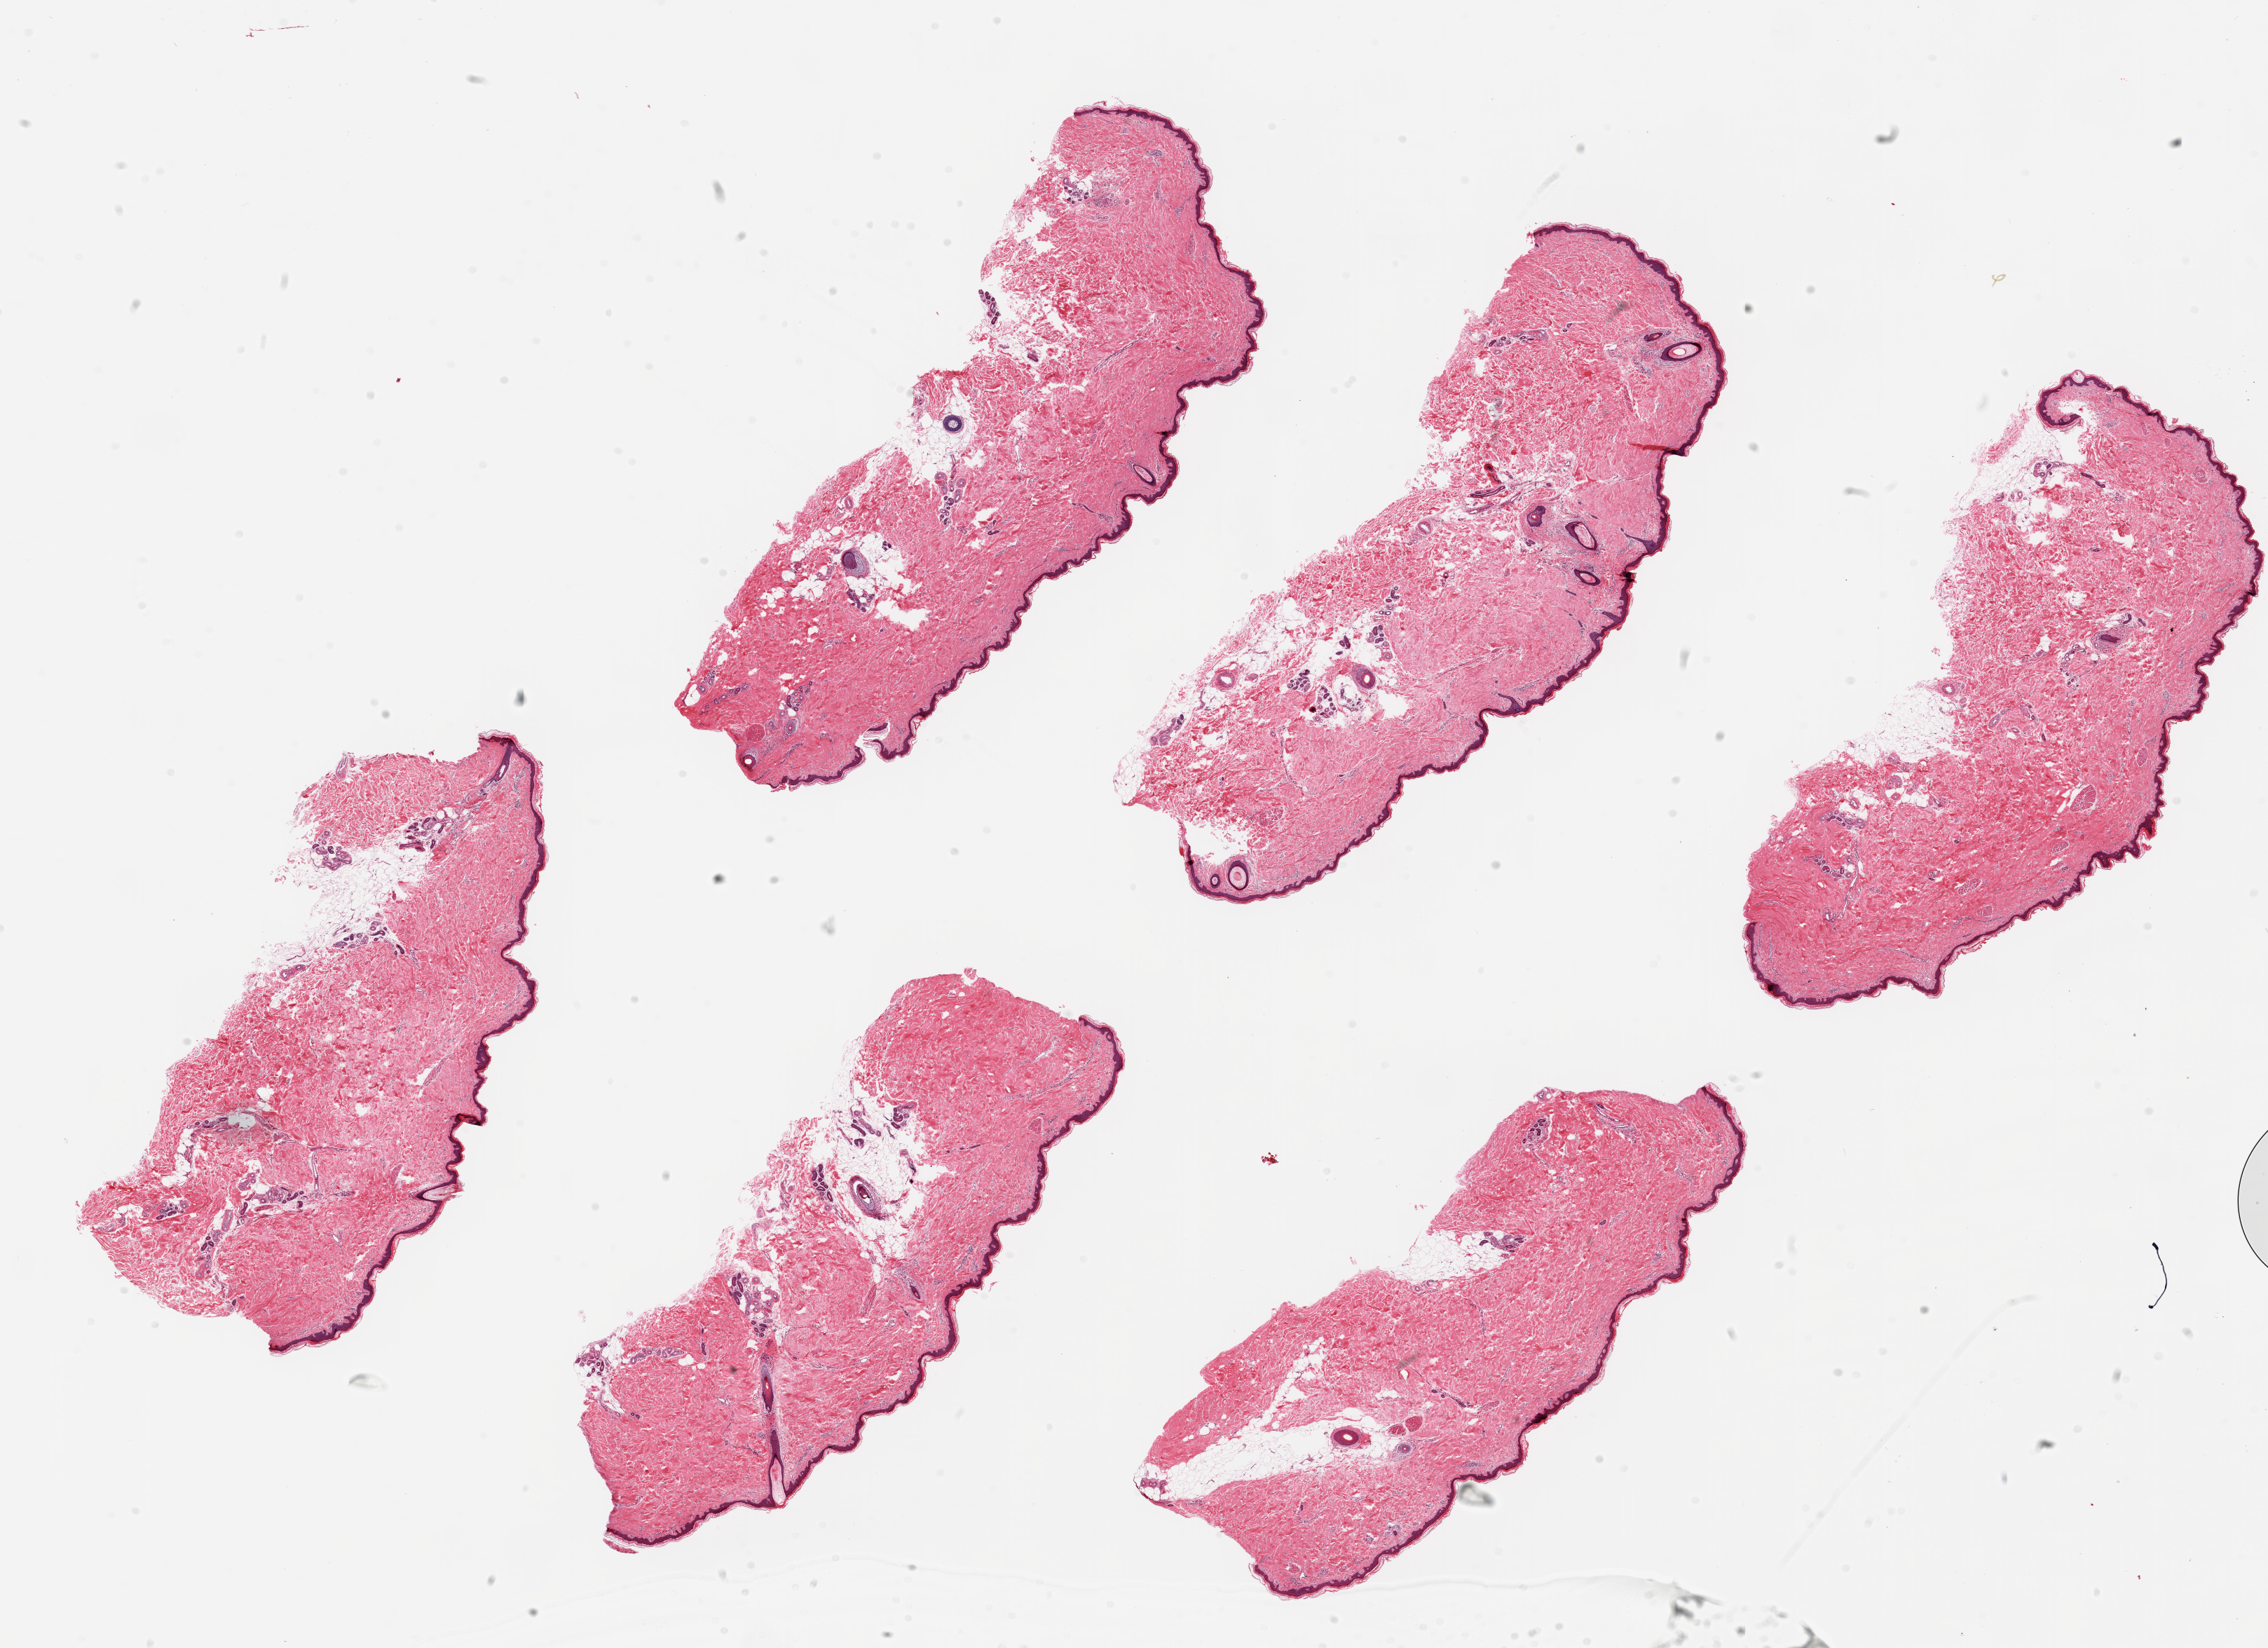
Haematoxylin and eosin whole-slide image, brightfield — a low-resolution overview of the entire scanned area, about 25.6 x 18.6 mm, PAXgene-fixed, paraffin-embedded tissue, target tissue: skin of lower leg, tissue donor sample. Donor sex: male.
Review note (as recorded): 6 pieces, ~7x3mm. Squamous epithelium is ~2-3% of thickness.